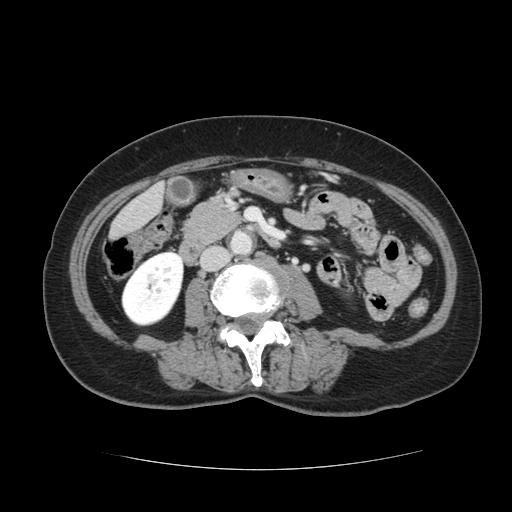
Contrast-enhanced abdominal CT, one axial slice; position 20 of 128 along the scan axis; 120 kVp; intravenous contrast given; soft-tissue window (W 400 / L 40 HU); 2.5 mm slice thickness; 512 × 512 image matrix, field of view 366 × 366 mm. Female patient, age 67 years. Case-level facts recorded for this patient, not image findings: diagnosis: colorectal cancer liver metastases, imaged before liver resection; multiple liver metastases: yes; largest metastasis: 3 cm; disease in both lobes: yes.
Annotated regions visible in this slice (manually delineated by an expert):
- liver: bounding box [x1, y1, x2, y2] px = [112, 187, 163, 238]
- planned liver remnant (the part of the liver to remain after resection): [112, 207, 143, 239]